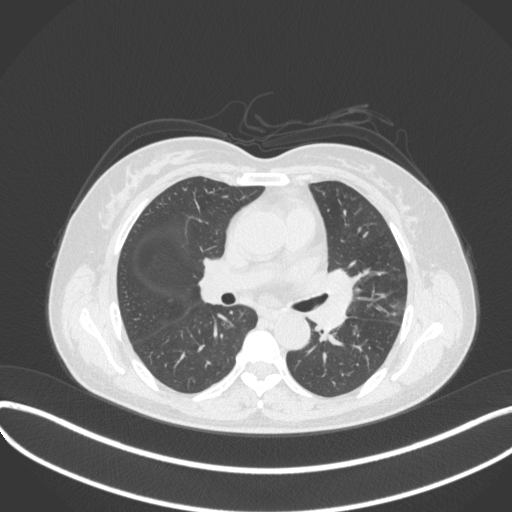
Chest CT, one axial slice. Slice 197 of 373 in the series (ordered by position). 120 kVp. Lung window (W 1500 / L -600 HU). 1 mm slice thickness. 512 × 512 image matrix. Patient: female, 54 years. From the clinical record (not read from this slice): clinical TNM (as recorded): T2a N1 M0; histopathological grade: G3.
Annotated regions visible in this slice (bounding box drawn by a radiologist):
- lung tumour (recorded histology: small cell carcinoma): bounding box <307,265,356,333> (left, top, right, bottom; pixels)